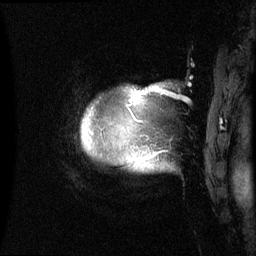
Breast MRI (dynamic contrast-enhanced), one sagittal slice. Dynamic contrast-enhanced series, image 2 of 3 at this slice position (ordered by acquisition). 1.5 T. TE 4.2 ms, TR 8.4 ms. 2.4 mm slice thickness. 256 × 256 image matrix, field of view 230 × 230 mm. Female patient, age 48 years.
Outlined on this slice (semi-automatically segmented with operator editing):
- analysis volume of interest (the breast-tissue region the enhancement analysis was run in; not a lesion): box from (x=82, y=86) to (x=158, y=169) px
- tumour enhancement mask (voxels above the 70 % enhancement threshold inside the analysis volume of interest): (x=137, y=92)–(x=152, y=159)